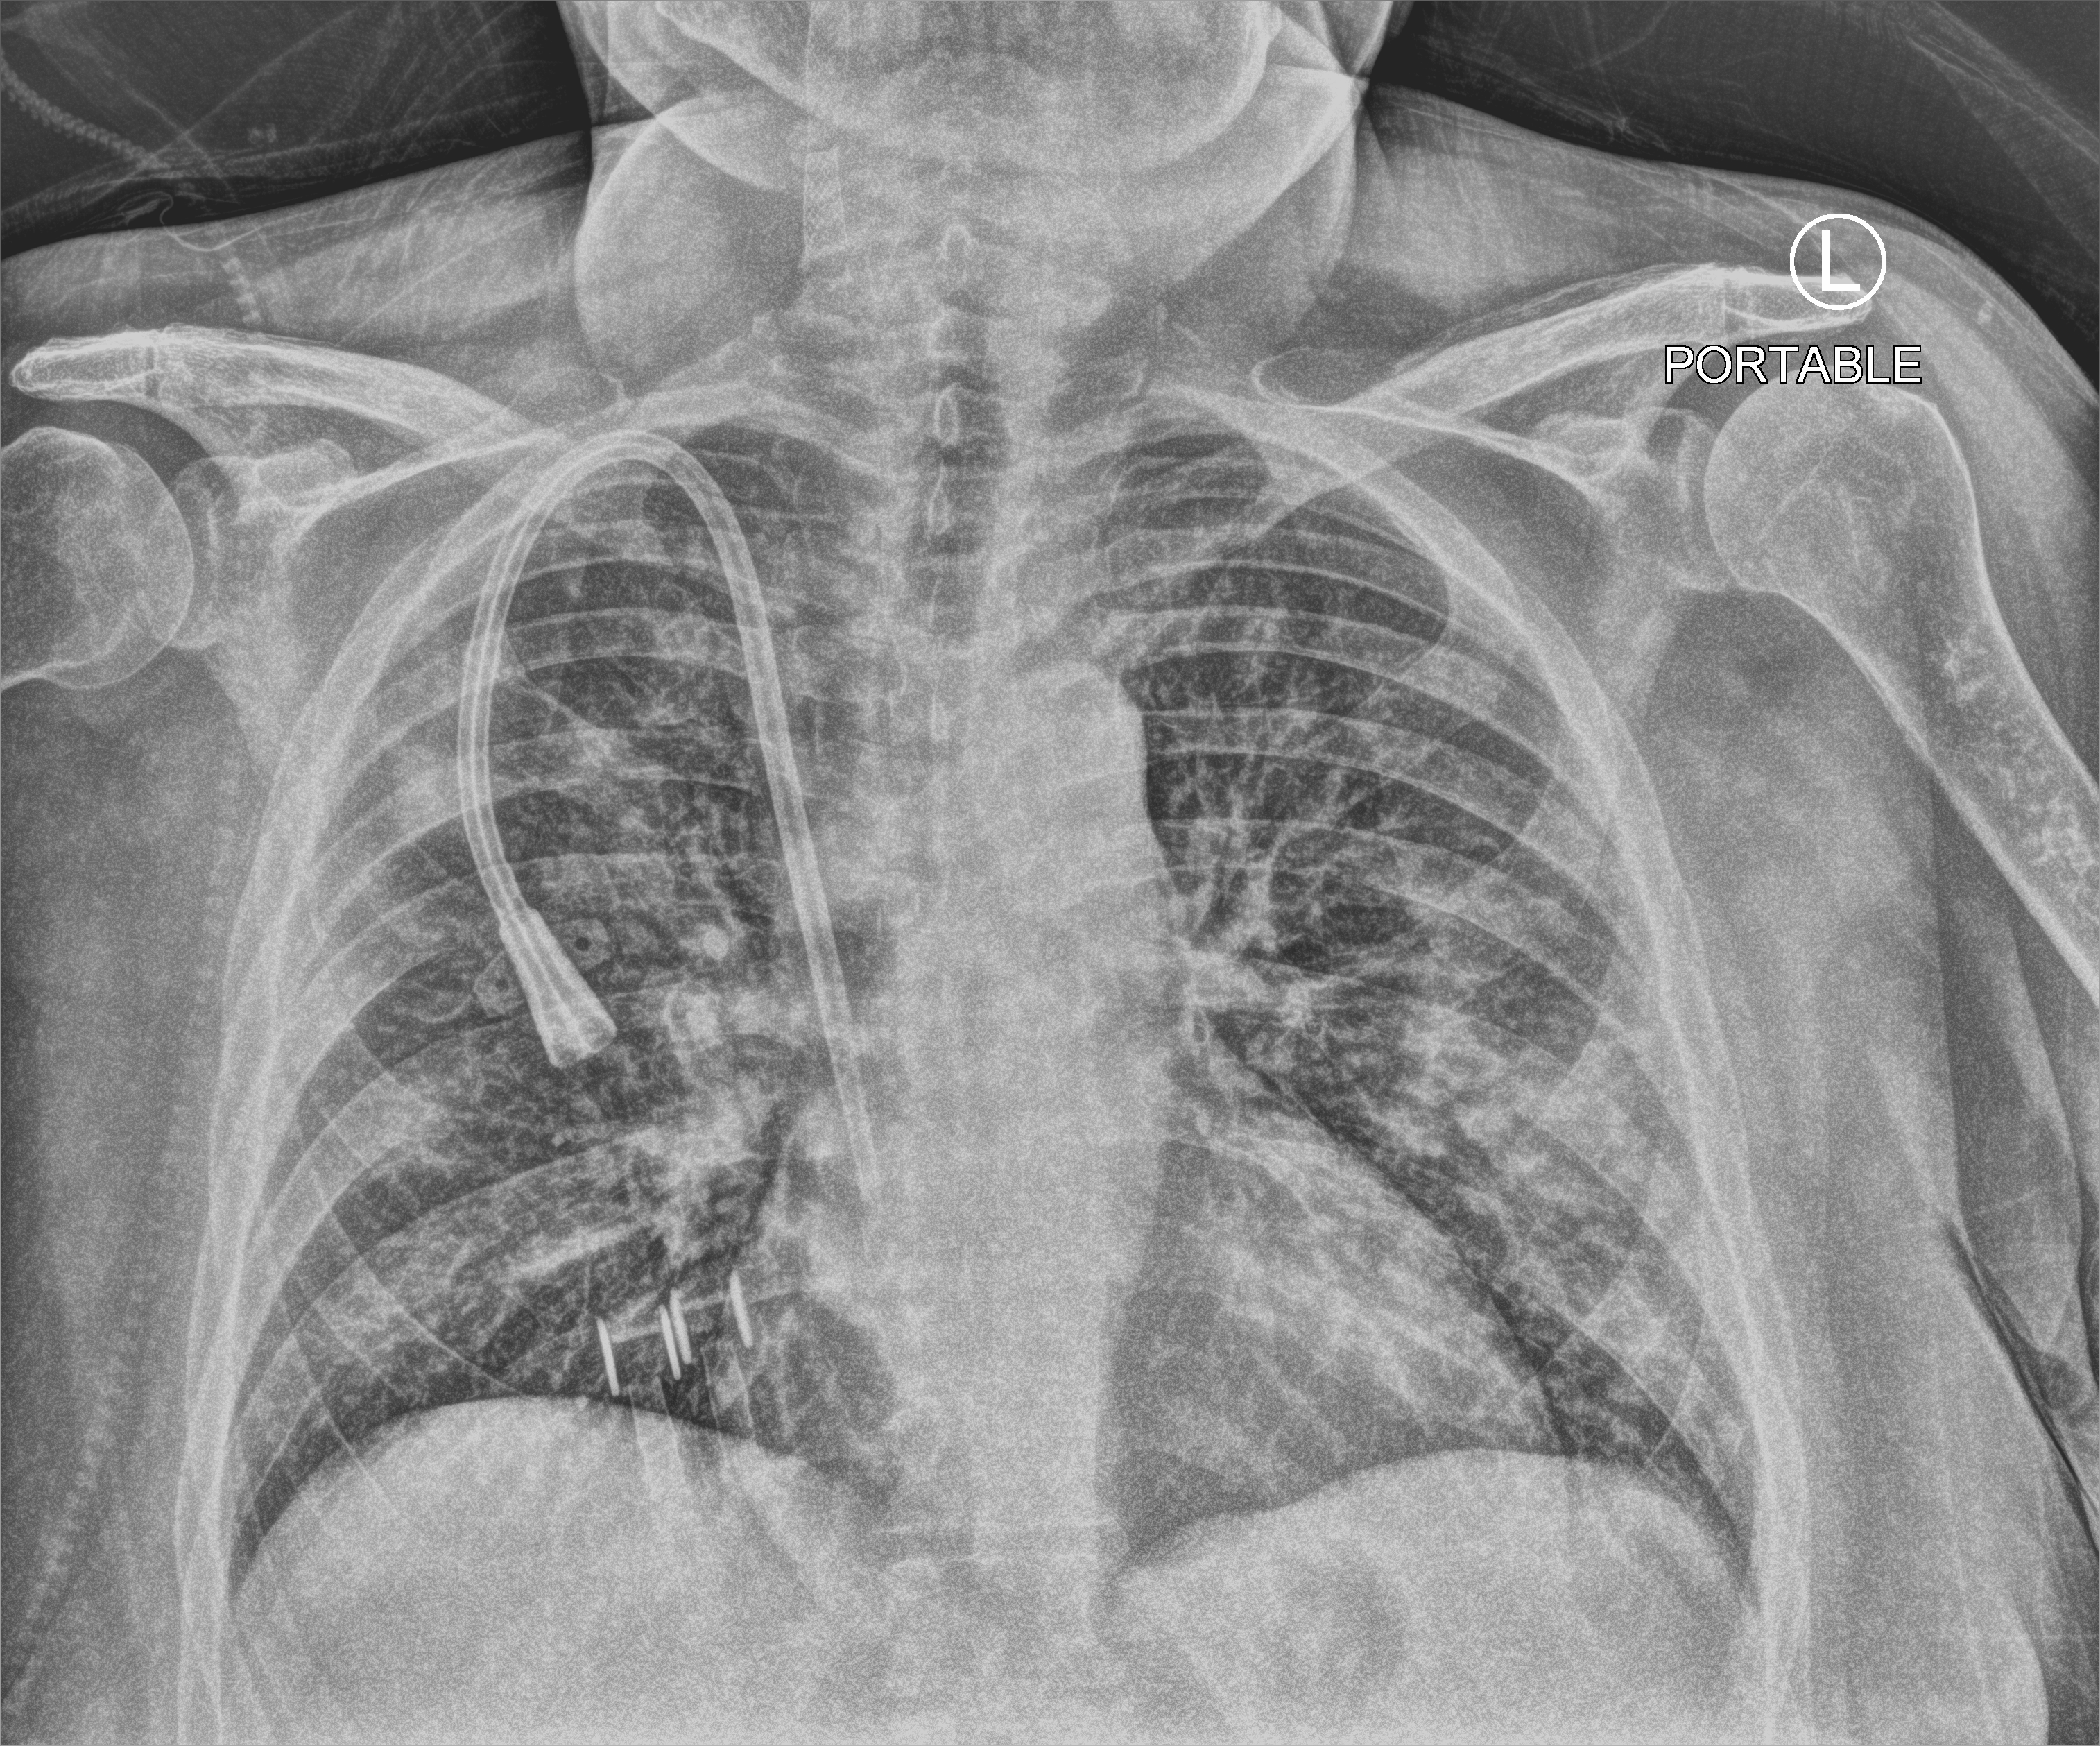
Bedside chest radiograph (computed radiography); anteroposterior (AP) projection. Patient hospitalised with COVID-19; female, aged 60–74 years.
Hospital-stay facts (about this admission, not read from this image; timing relative to this image not recorded): length of hospital stay: 8 days.